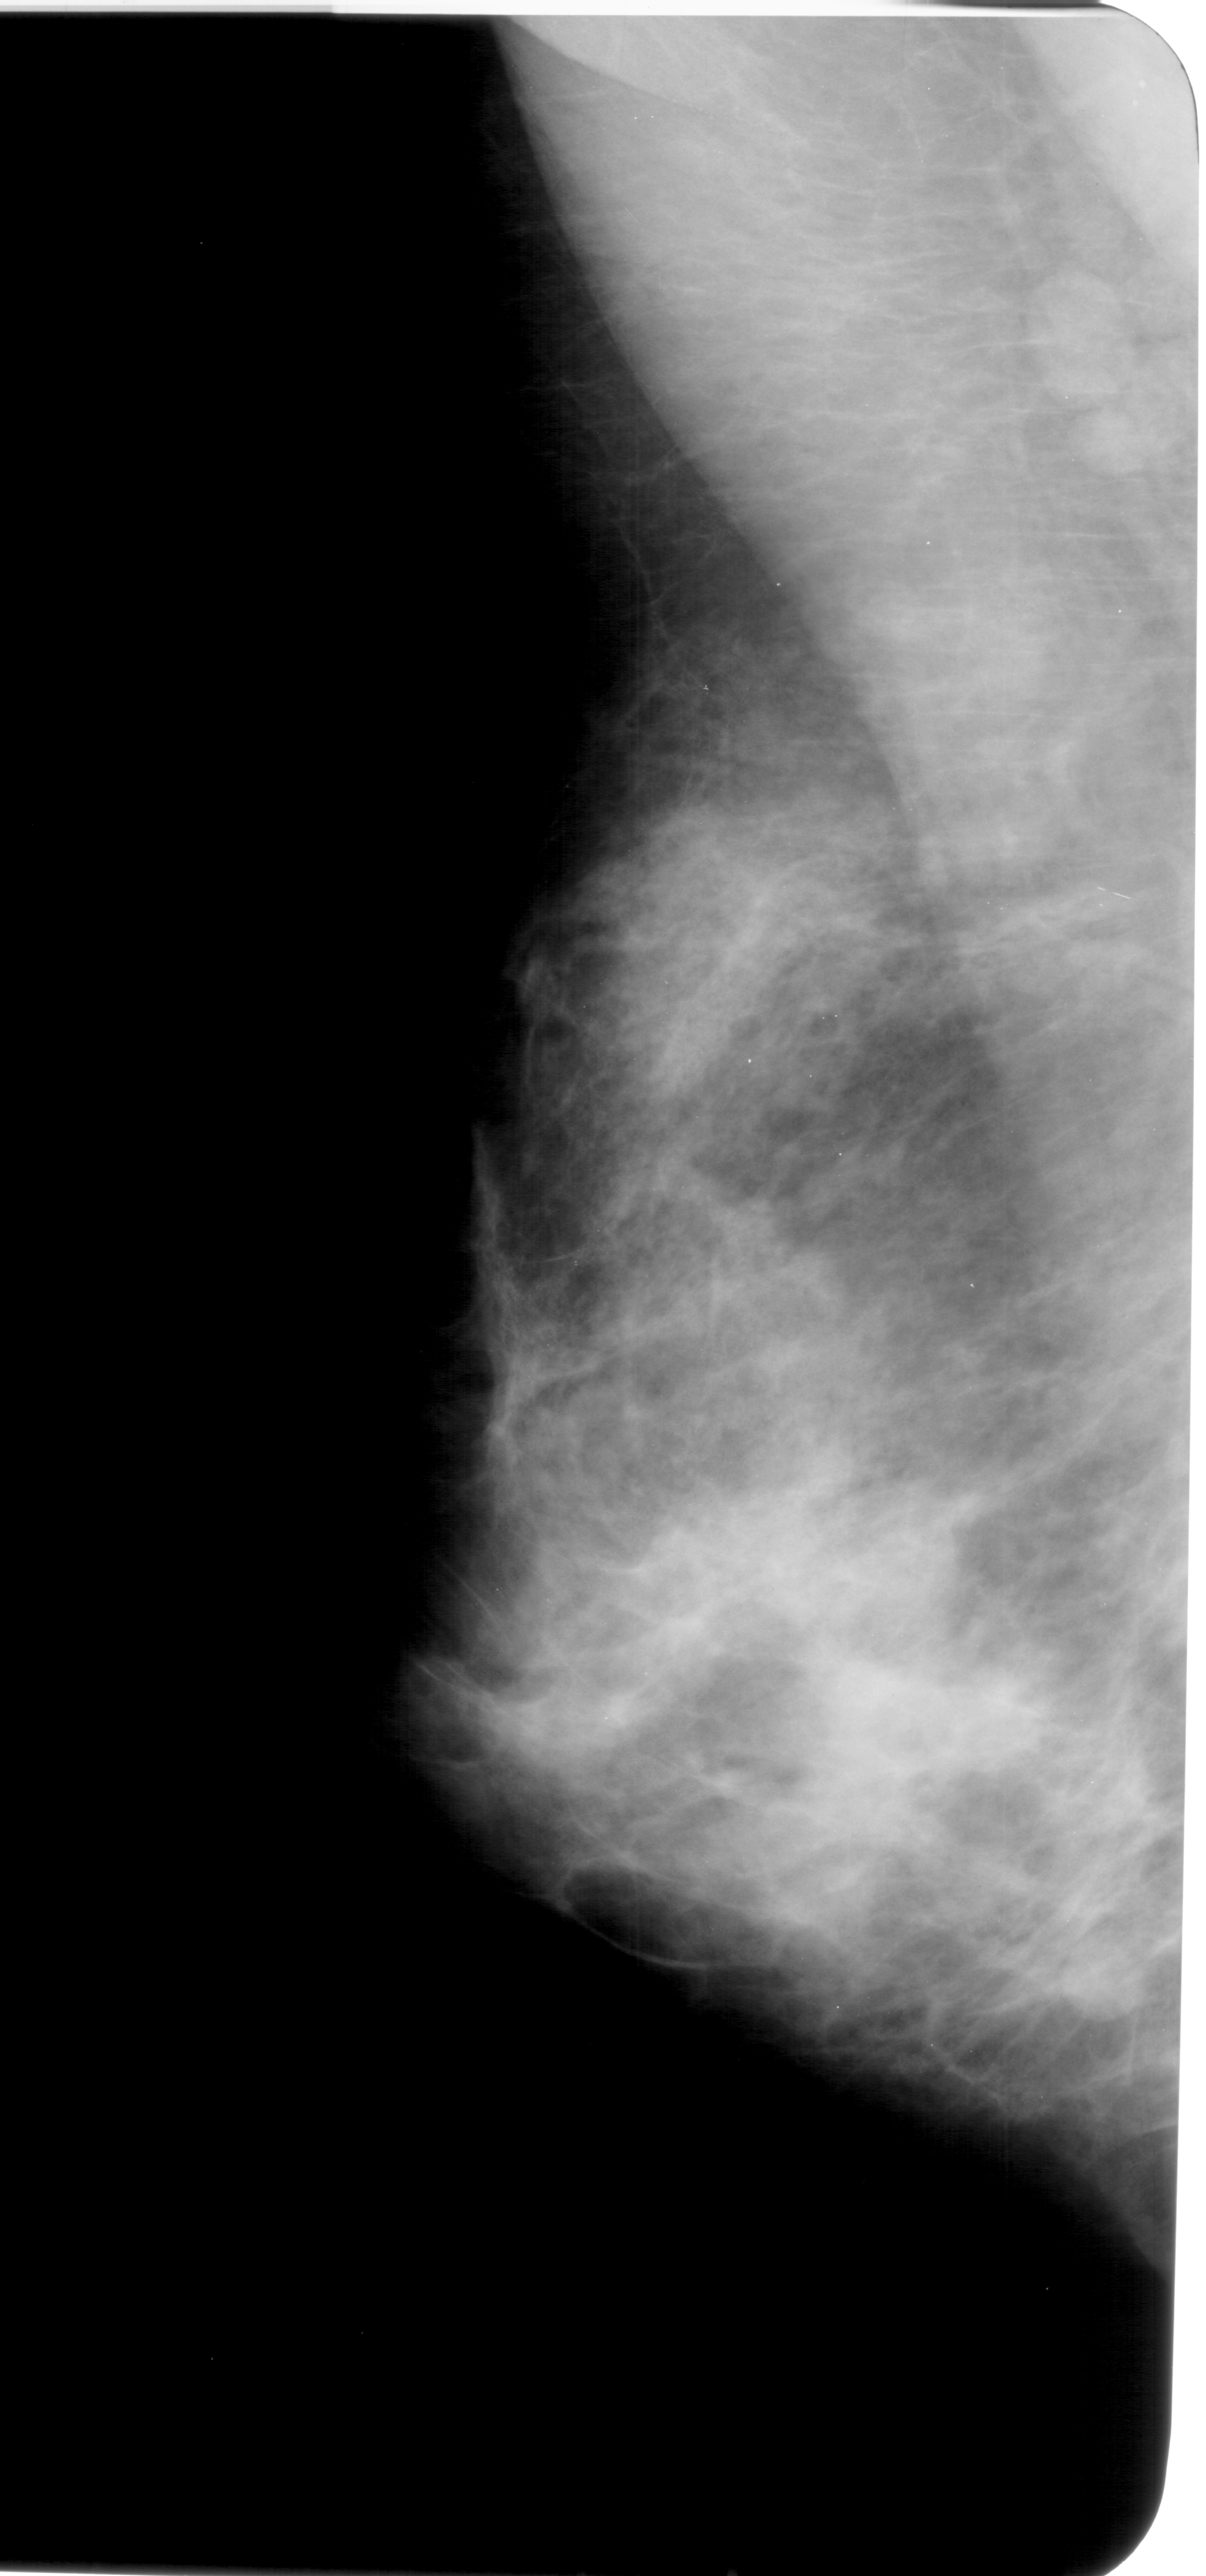
Scanned film-screen mammogram. Left breast. Mediolateral oblique (MLO) view. BI-RADS breast density category 4 (scale 1–4). 1206 × 2576 image matrix.
Expert-marked regions of interest on this image (one box per marked abnormality):
- mass, shape round, margins circumscribed; BI-RADS assessment category 4; pathology (as recorded): benign: bounding box <999,1908,1185,2077> (left, top, right, bottom; pixels)